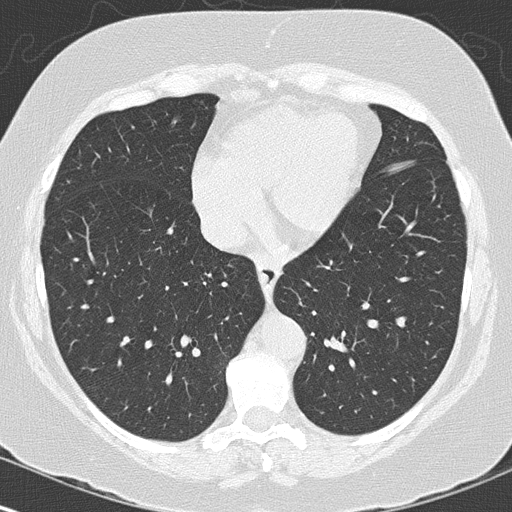
Chest CT (low-dose screening protocol), one axial image; baseline annual screen; lung window (W 1500 / L -600 HU); 2 mm slice thickness; lung (sharp) reconstruction kernel (B50f); 120 kVp; slice 94 of 144 in the series. Female, age 60 years at enrolment. Former smoker at enrolment.
Lesion marked by an expert reader, bounding box [x1, y1, x2, y2] px = [346, 292, 388, 327]. Screening reader's record for this exam (one nodule recorded; not confirmed to be the boxed lesion): non-calcified nodule or mass ≥4 mm, left lower lobe, 12 × 10 mm, smooth margins, soft tissue attenuation. Official screen result: positive, change unspecified: nodule(s) >= 4 mm or enlarging nodule(s), mass(es), or other non-specific abnormalities suspicious for lung cancer.